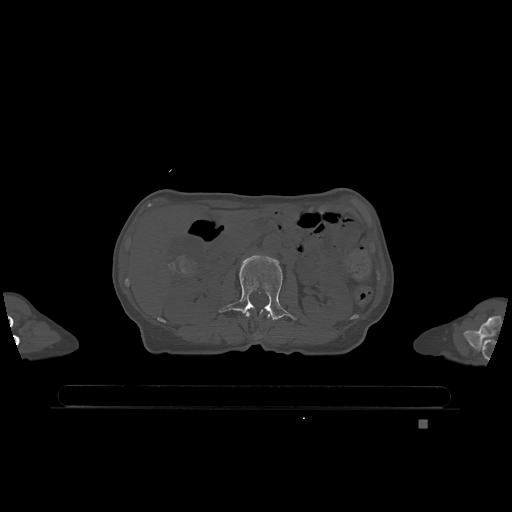
CT including the spine, one axial slice; slice 423 of 1317 in the series (ordered by position); bone window (W 1800 / L 400 HU); 0.5 mm slice thickness; 512 × 512 image matrix. Patient: female, 74 years. From the clinical record (not read from this slice): primary cancer: lung; vertebrae with lytic lesions (as recorded): T1, T4, T5, T6, L4, L5.
Annotated regions visible in this slice (semi-automatically segmented with operator editing):
- L1 vertebra: box from (x=244, y=312) to (x=270, y=336) px
- L2 vertebra: (x=218, y=255)–(x=296, y=321)